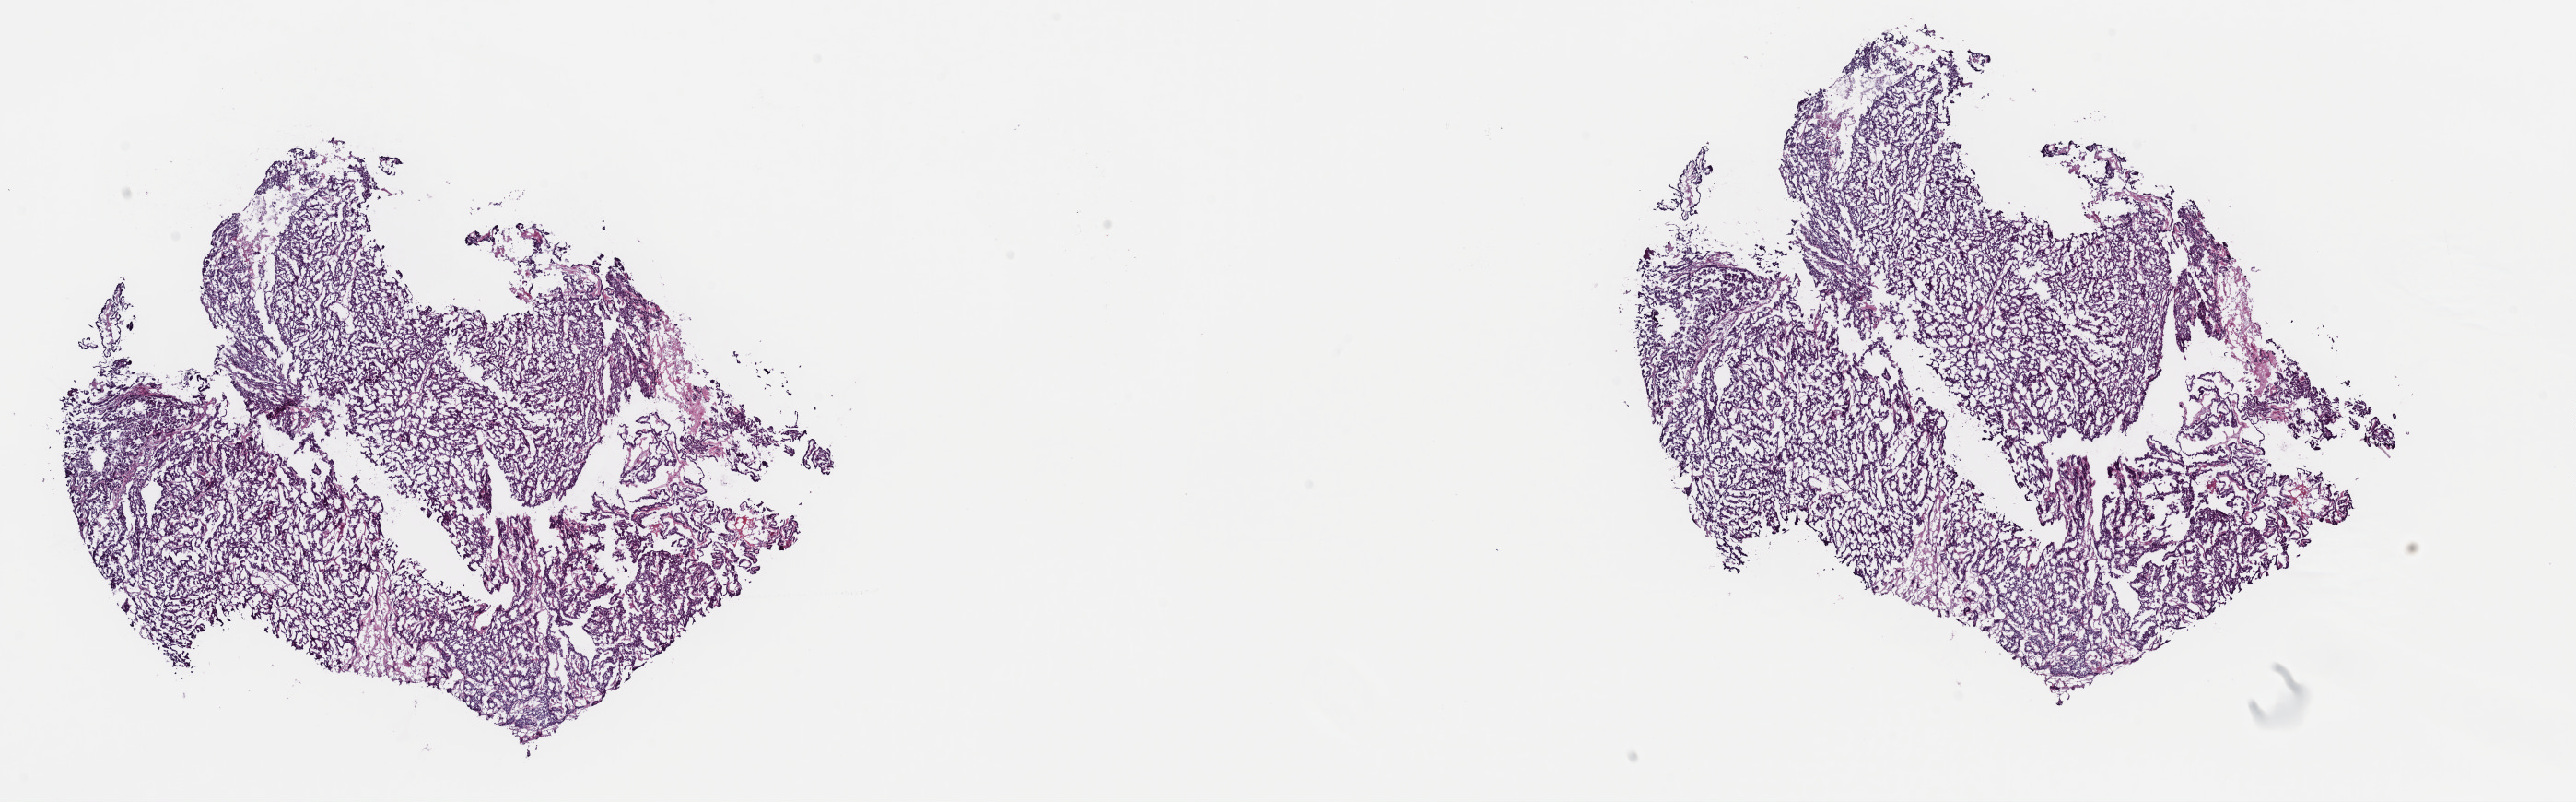
Whole-slide histology image, H&E-stained, whole scanned area (about 22.1 x 6.9 mm, slide scanned at 40x) shown as a low-resolution overview. Frozen section from the top of the tissue portion. Thyroid, primary tumour sample. Patient: female, age at initial diagnosis 66 years. Composition of this section per pathologist review: tumour cells 90%, tumour nuclei 100%, normal cells 0%, stromal cells 10%, necrosis 0%. Infiltration values recorded for this section: lymphocyte infiltration 0%, monocyte infiltration 2%, neutrophil infiltration 0%.
- histologic diagnosis: Papillary adenocarcinoma, NOS (thyroid gland)
- lymph nodes positive (case pathology): 0 of 2 examined
- AJCC pathologic stage: IVC (6th edition)